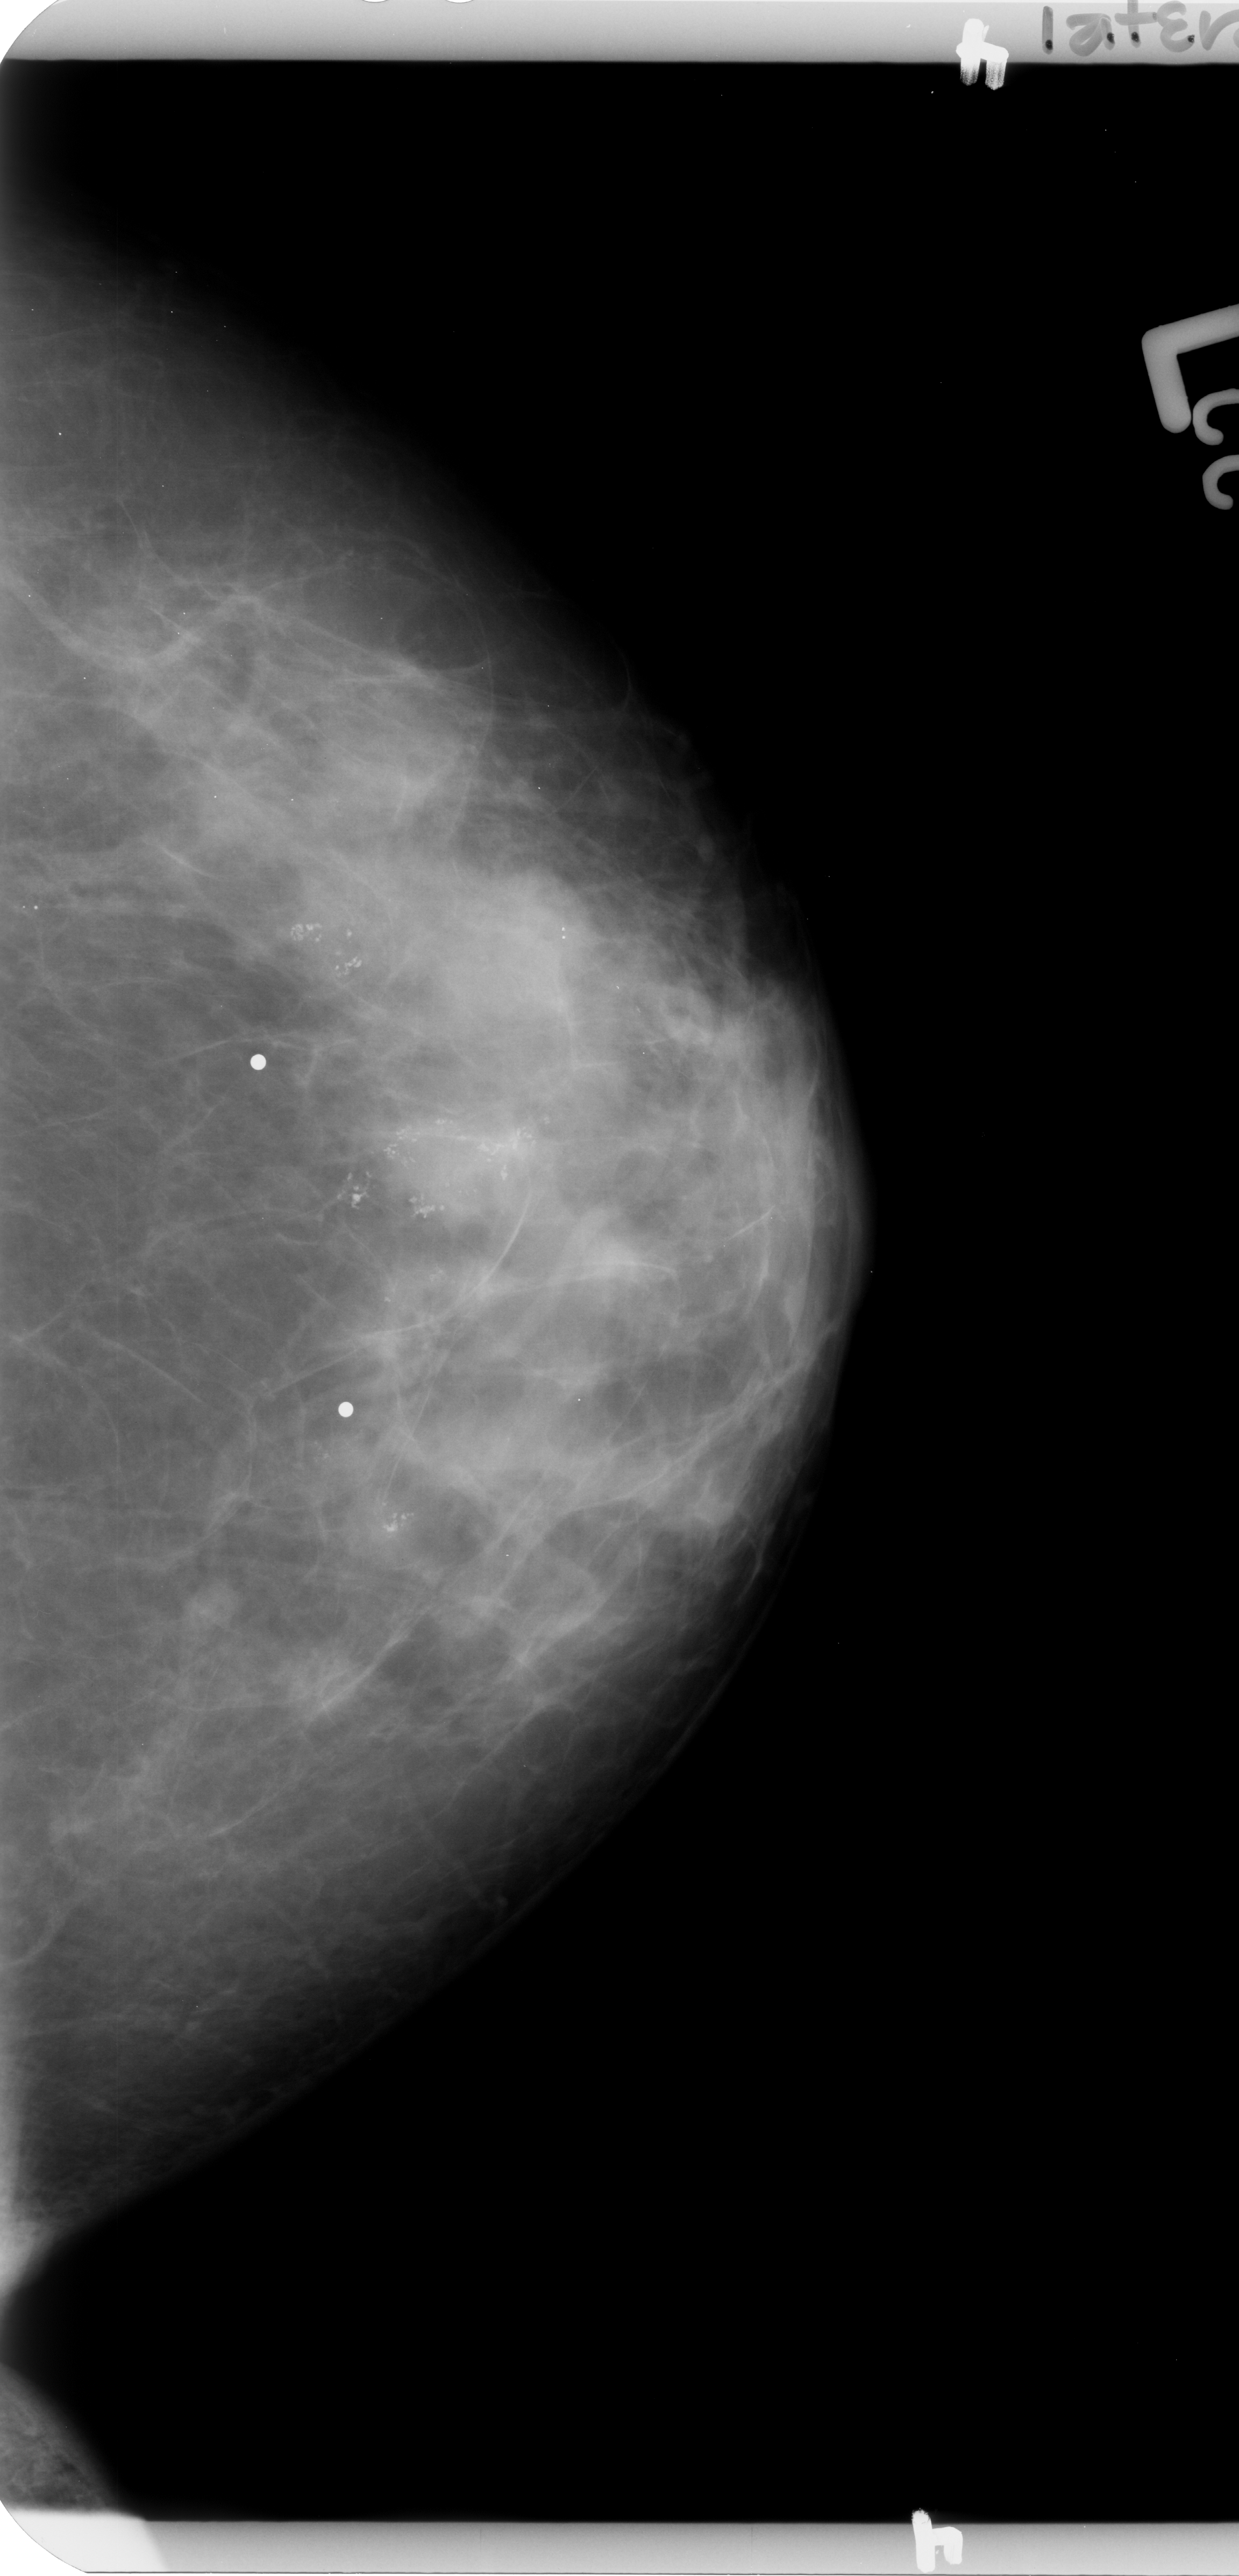
Mammogram (digitized film). Left breast. CC view. BI-RADS breast density category 3 (scale 1–4). 1239 × 2576 image matrix.
Marked abnormalities (boxes around the expert regions of interest):
- Finding 1 of 3: calcifications, morphology pleomorphic, distribution clustered / segmental; BI-RADS assessment category 4; subtlety rating 4 on a 1 (subtle) to 5 (obvious) scale; pathology (as recorded): benign: bounding box (x1, y1, x2, y2) in pixels: (249, 894, 401, 1016)
- Finding 2 of 3: calcifications, morphology pleomorphic, distribution clustered / segmental; BI-RADS assessment category 4; pathology (as recorded): benign: (266, 1087, 569, 1257)
- Finding 3 of 3: calcifications, morphology pleomorphic, distribution clustered / segmental; BI-RADS assessment category 4; pathology (as recorded): benign: (344, 1470, 448, 1575)